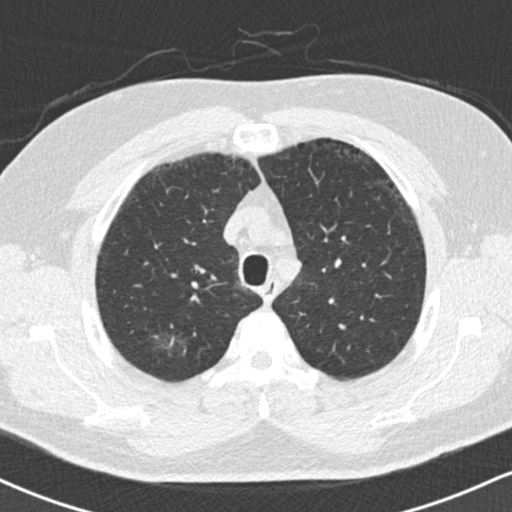
Low-dose screening chest CT, one axial slice; slice 131 of 169 in the series (ordered by position); reconstruction kernel B30f; lung window (W 1500 / L -600 HU); 2 mm slice thickness; 512 × 512 image matrix, field of view 320 × 320 mm.
Annotated regions visible in this slice (manually delineated by an expert):
- lesion 1 (tumor, upper lobe of right lung): bounding box [x1, y1, x2, y2] px = [153, 328, 186, 359]